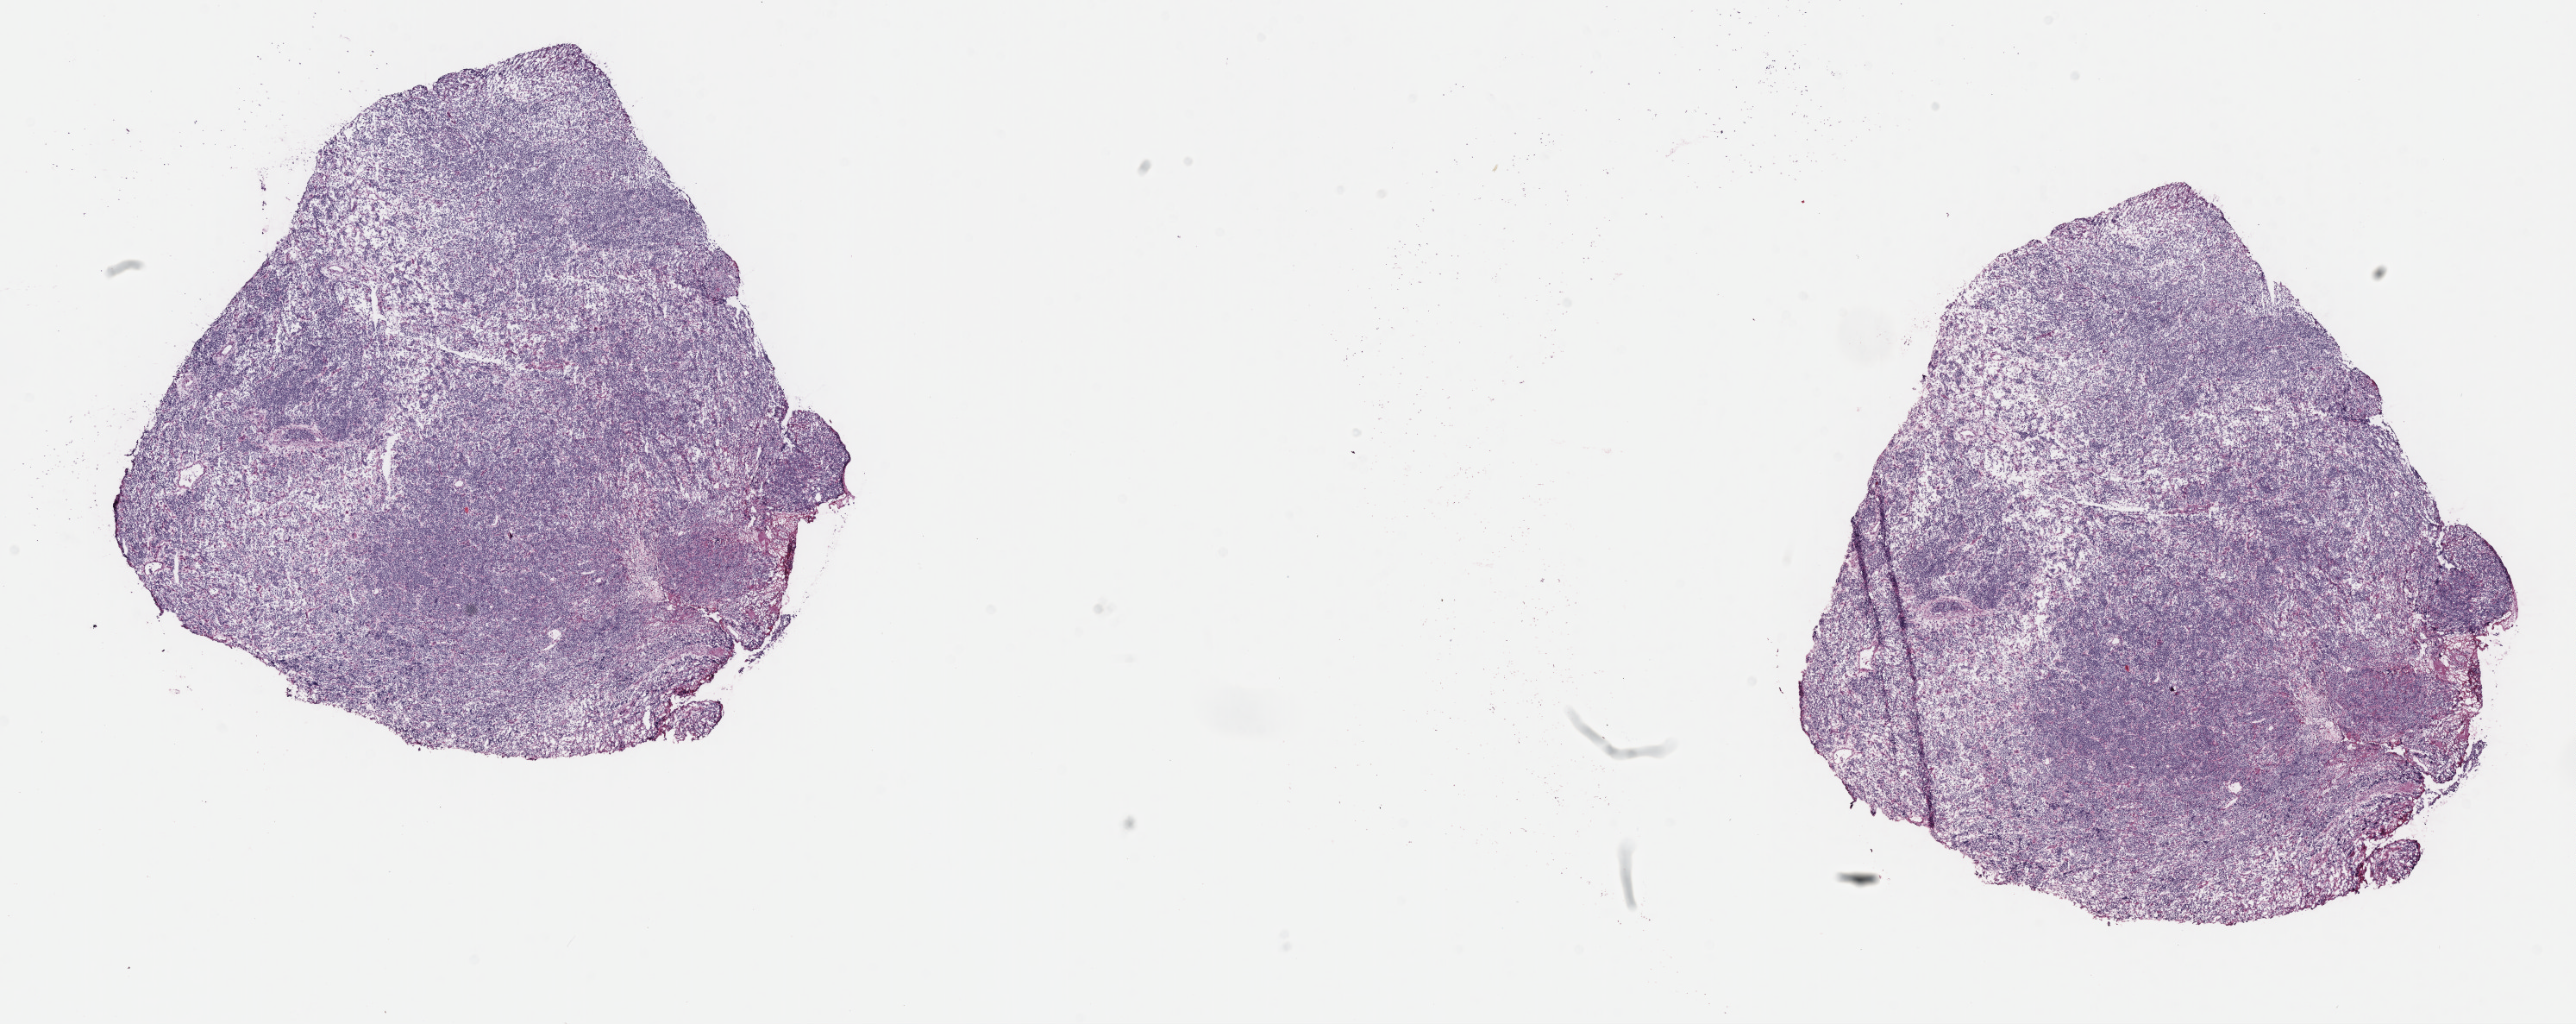
Digitized H&E-stained section, a low-resolution overview of the entire scanned area, about 24.2 x 9.6 mm; frozen section (tissue freezing medium); specimen: primary tumor; site: cranium. Male, age 5 years at initial diagnosis. Composition of this section per pathologist review: tumor cells 90%, tumor nuclei 90%, stromal cells 7%, necrosis 3%, normal cells 0%. Infiltration values recorded for this section: lymphocyte infiltration 3%, monocyte infiltration 3%, neutrophil infiltration 1%.
• Ann Arbor stage (patient): Stage III
• diagnosis: Burkitt lymphoma, NOS
• section: bottom of the tissue portion